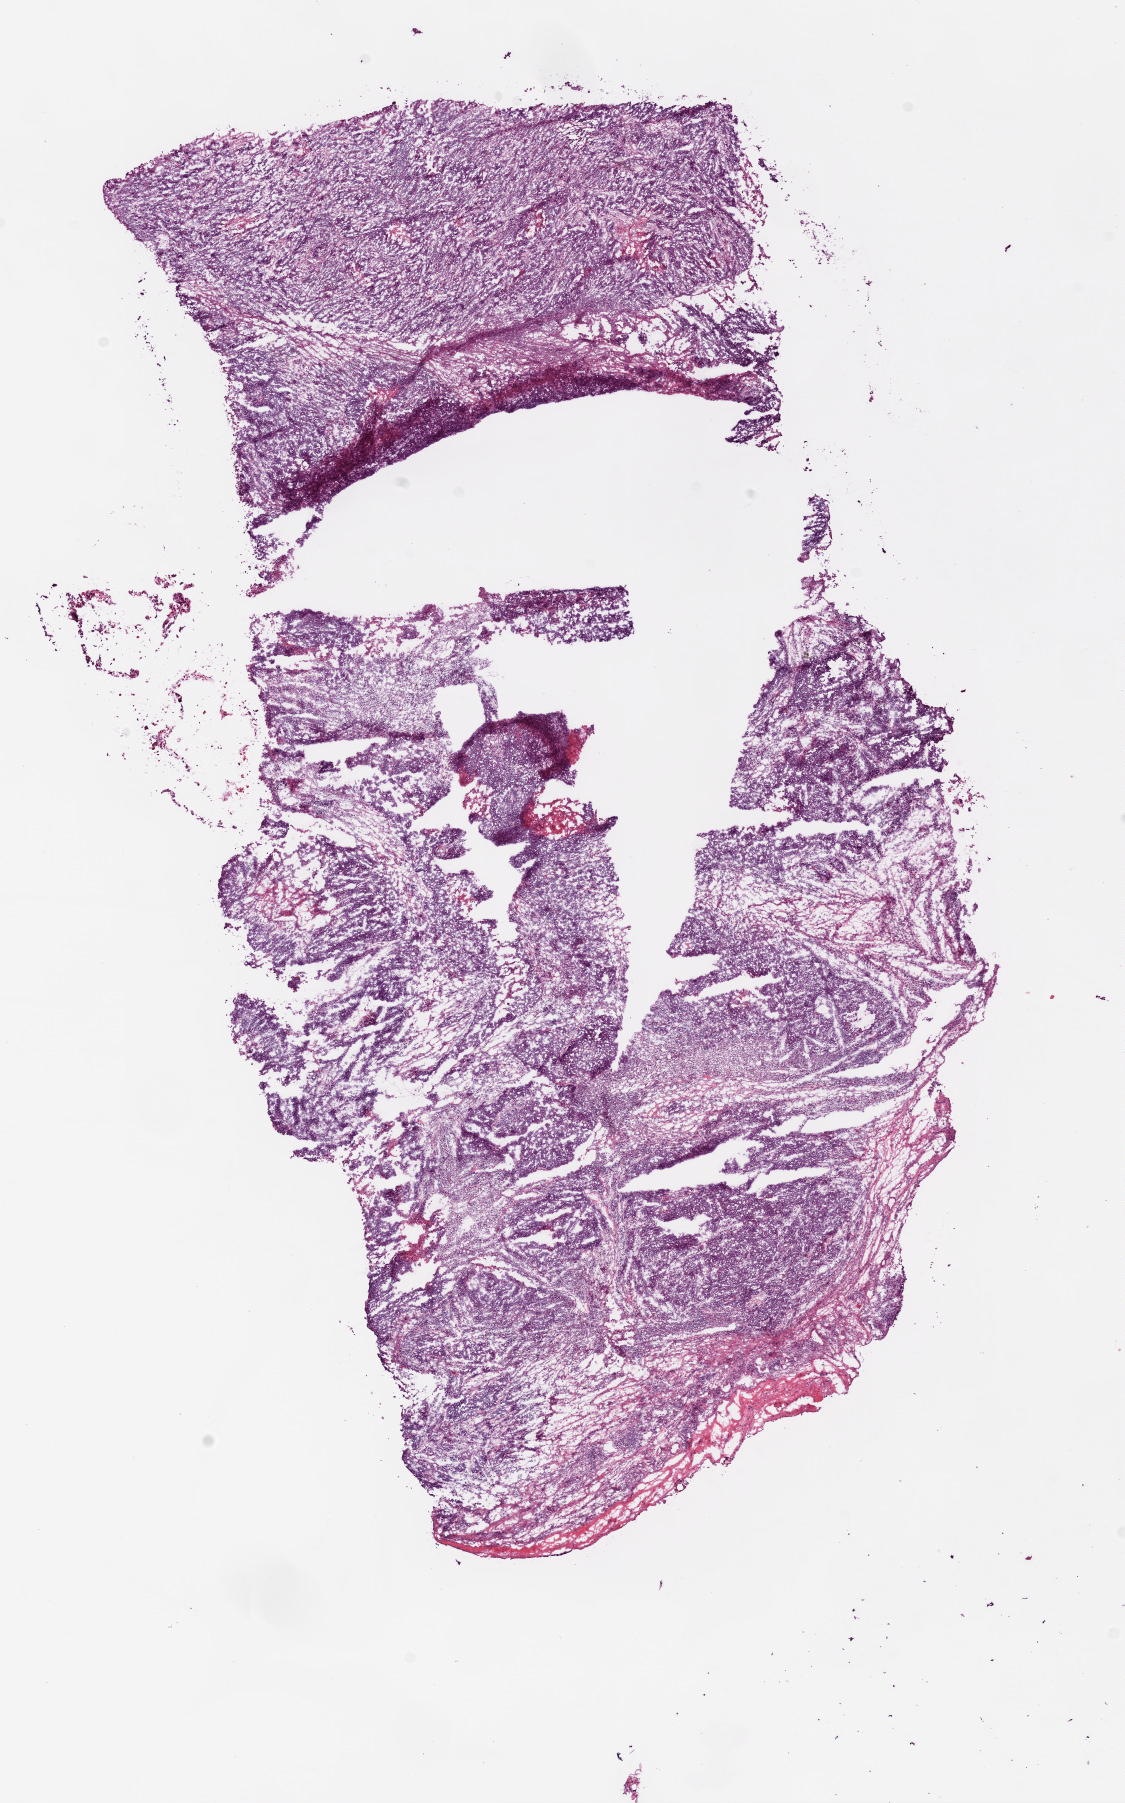
Whole-slide histology image, H&E — whole scanned area (about 9.0 x 14.5 mm, from a 20x scan) shown as a low-resolution overview, frozen section from the bottom of the tissue portion, primary tumour sample from the ovary. Female patient; age at initial diagnosis 79 years. Histologic grade: G3 (poorly differentiated). Slide review estimates, as recorded: tumour cells 85%, tumour nuclei 95%, normal cells 0%, stromal cells 10%, necrosis 5%.
FIGO stage: IIIC. Pathologic diagnosis: Serous cystadenocarcinoma, NOS. Laterality: right.